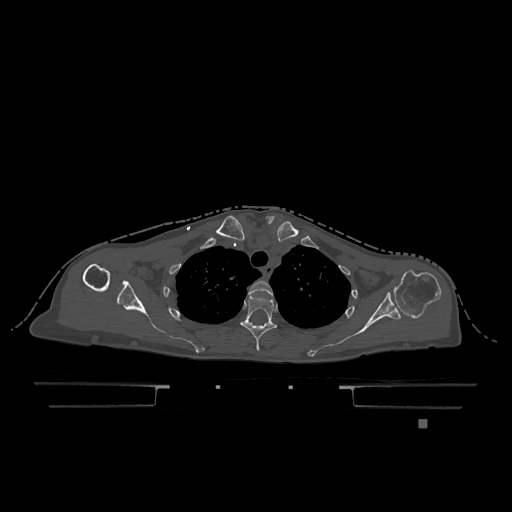
CT including the spine, one axial slice; position 926 of 1317 along the scan axis; bone window (W 1800 / L 400 HU); 512 × 512 image matrix. Female patient, age 74 years. From the clinical record (not read from this slice): primary cancer: lung.
Annotated regions visible in this slice (semi-automatically segmented with operator editing):
- T2 vertebra: box from (x=248, y=281) to (x=273, y=296) px
- T3 vertebra: (x=240, y=296)–(x=277, y=351)